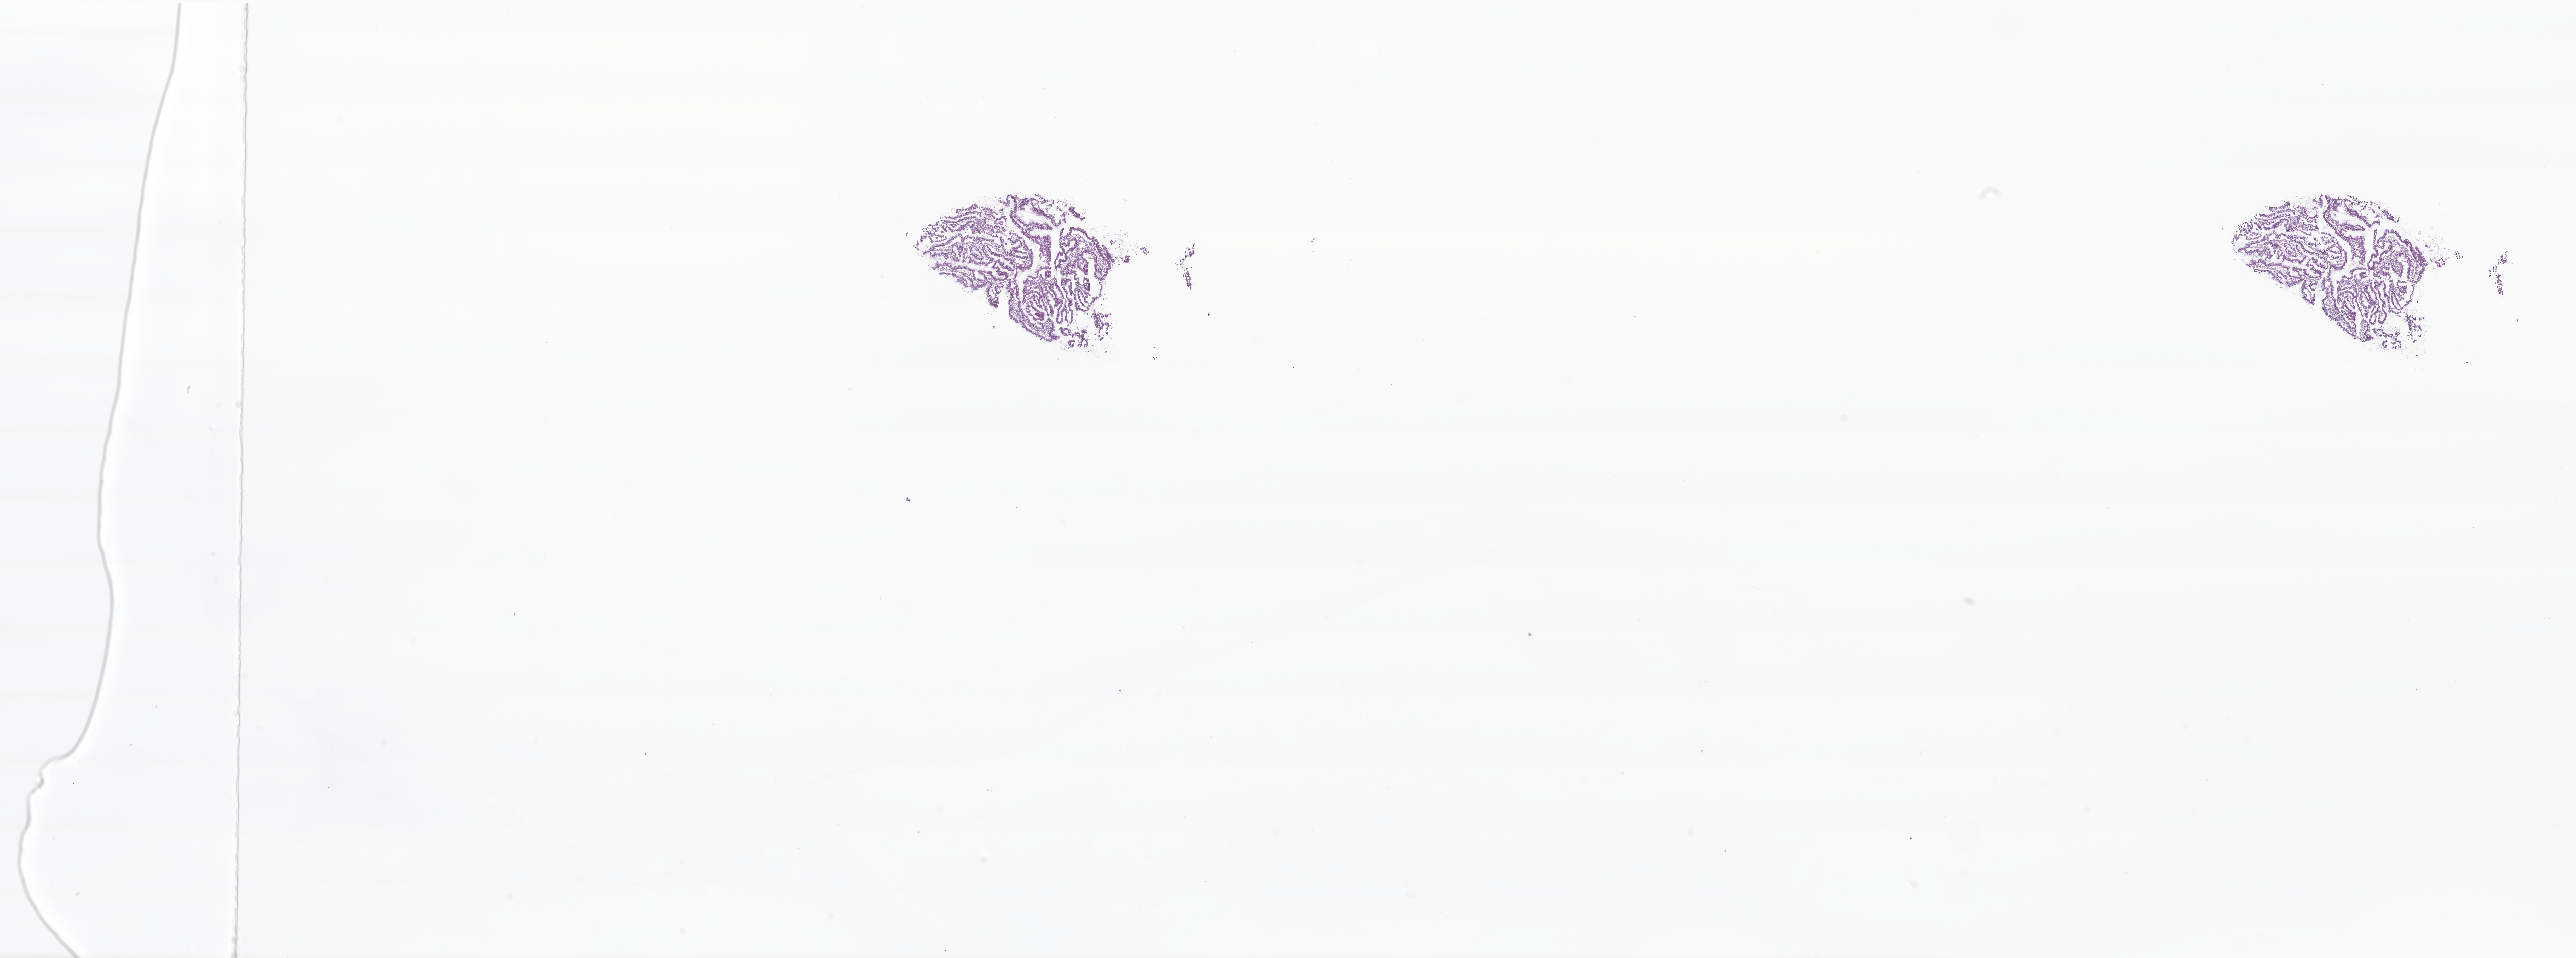
Hematoxylin and eosin (H&E) whole-slide image, shown as a low-resolution overview of the whole scanned area (about 41.6 x 15.5 mm). Frozen section (tissue freezing medium). Primary tumor. Anatomic site: rectosigmoid junction. Female patient. Tumor grade: G1 (well differentiated). Slide review estimates, as recorded: tumor cells 60%, tumor nuclei 60%, stromal cells 40%, necrosis 0%, normal cells 0%. Infiltration values recorded for this section: lymphocyte infiltration 100%, monocyte infiltration 0%, neutrophil infiltration 0%.
• section: bottom of the tissue portion
• histologic diagnosis: Adenocarcinoma, NOS
• AJCC pathologic stage: Stage I